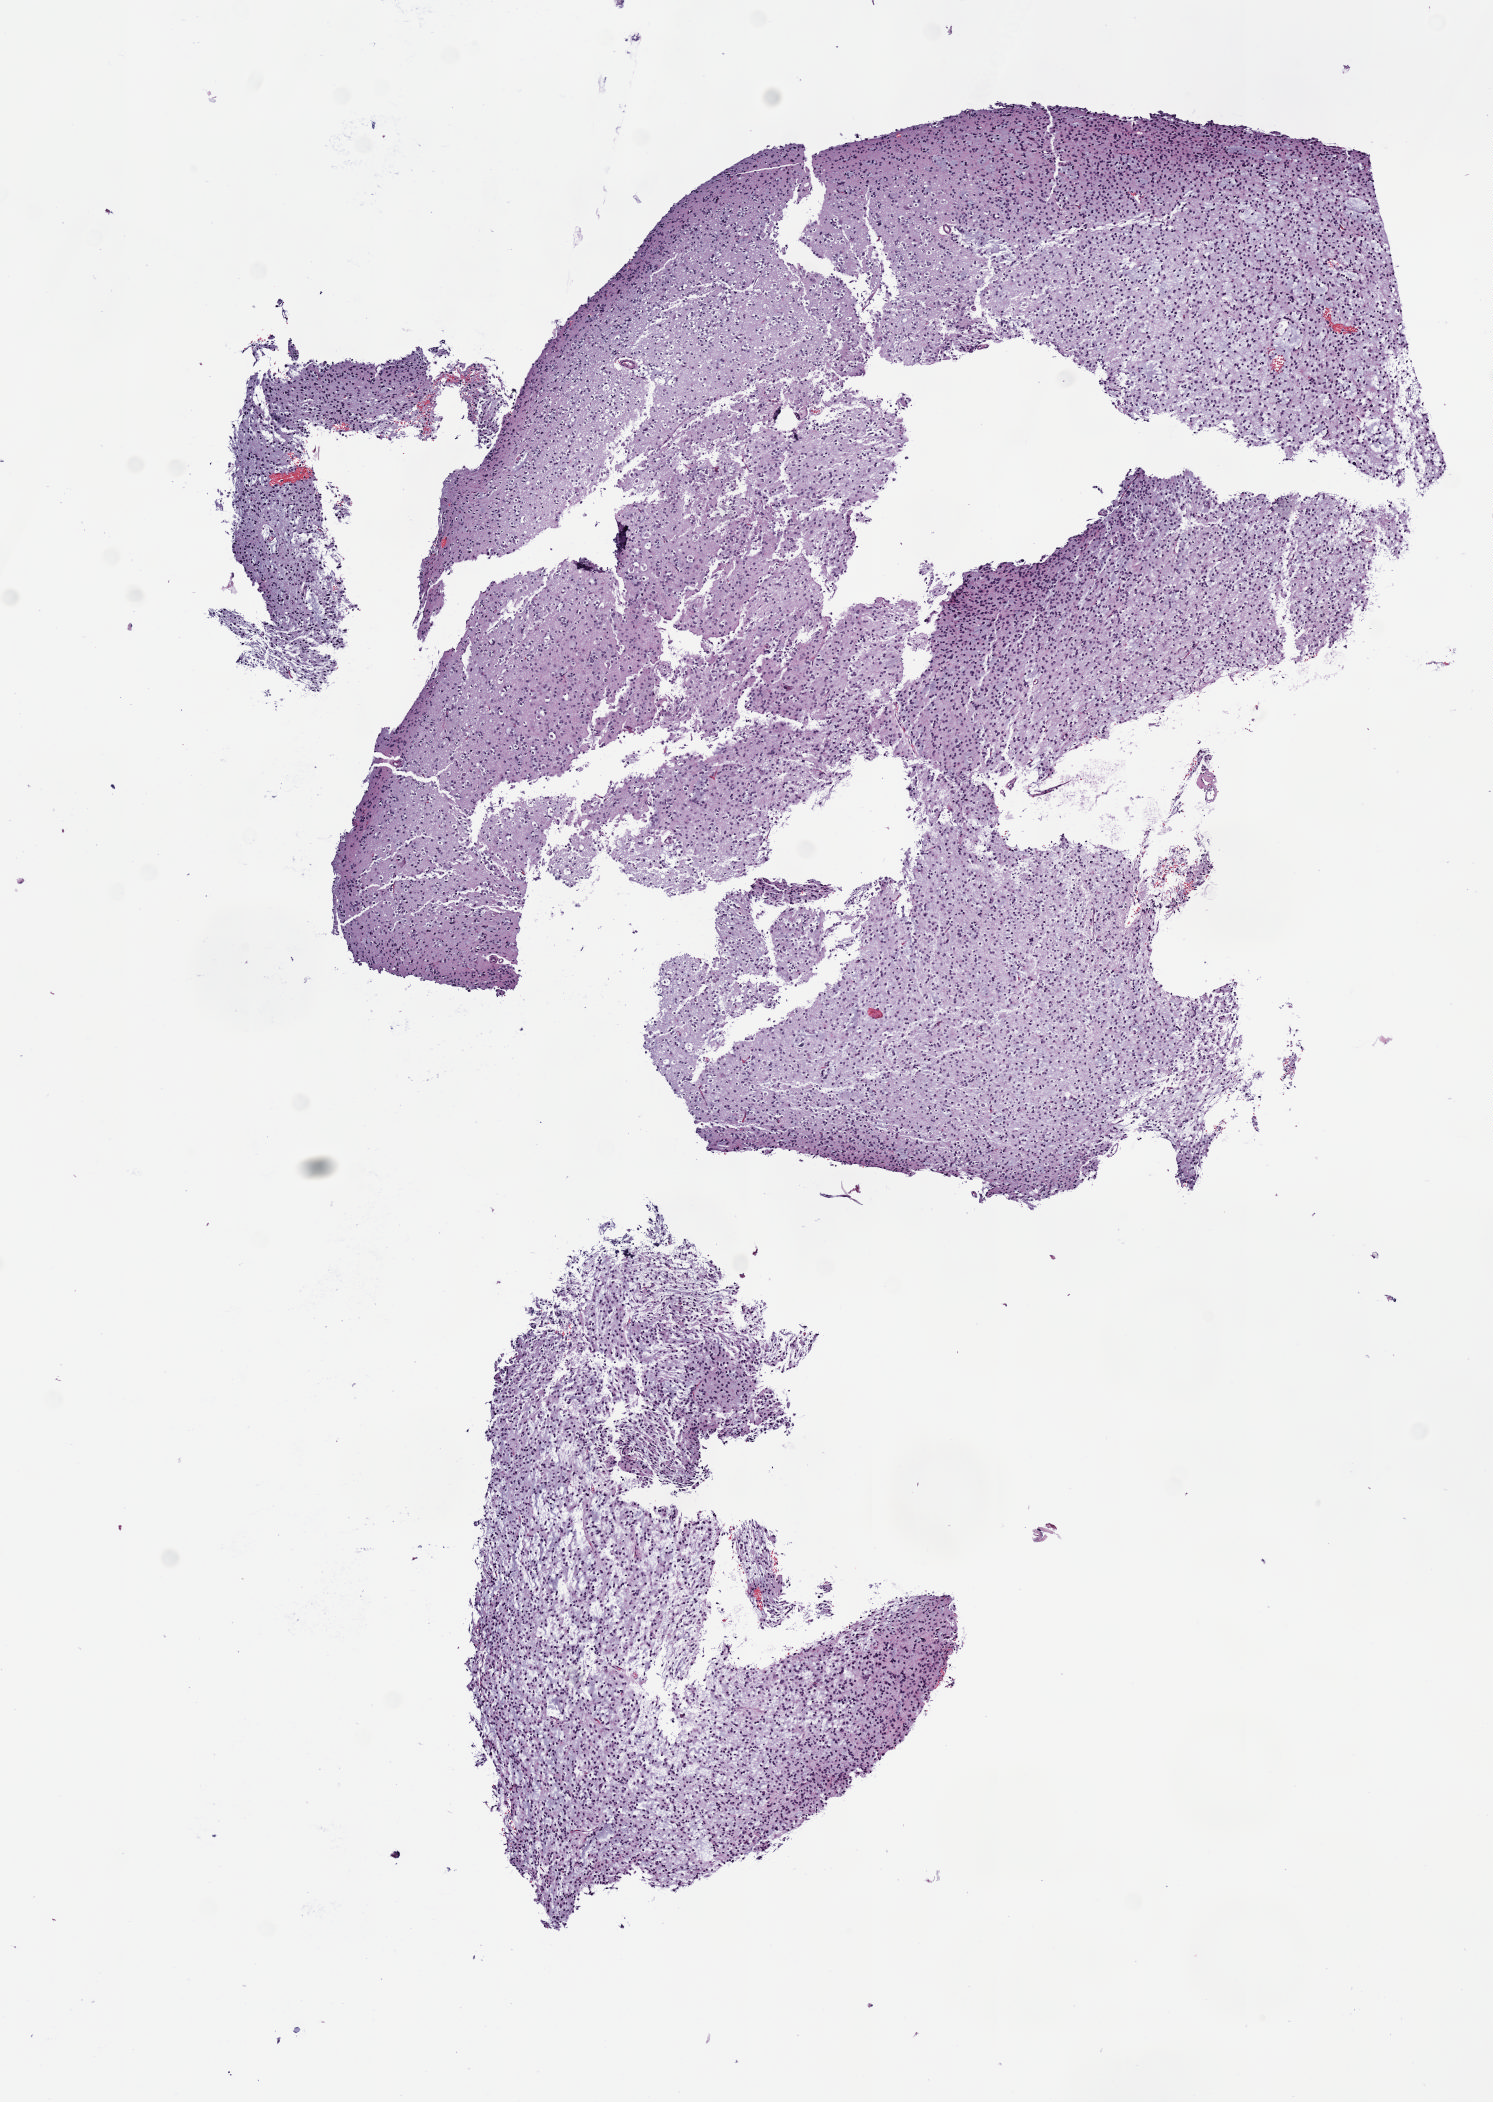
Whole-slide histology image, Hematoxylin and eosin (H&E) stained, whole scanned area (about 6.0 x 8.5 mm, acquisition: 40x scan) shown as a low-resolution overview, formalin-fixed paraffin-embedded (FFPE) diagnostic section, brain, primary tumour sample. Female patient; age at initial diagnosis 50 years. Histologic grade: G2 (moderately differentiated).
* laterality: right
* pathologic diagnosis: Oligodendroglioma, NOS (cerebrum)